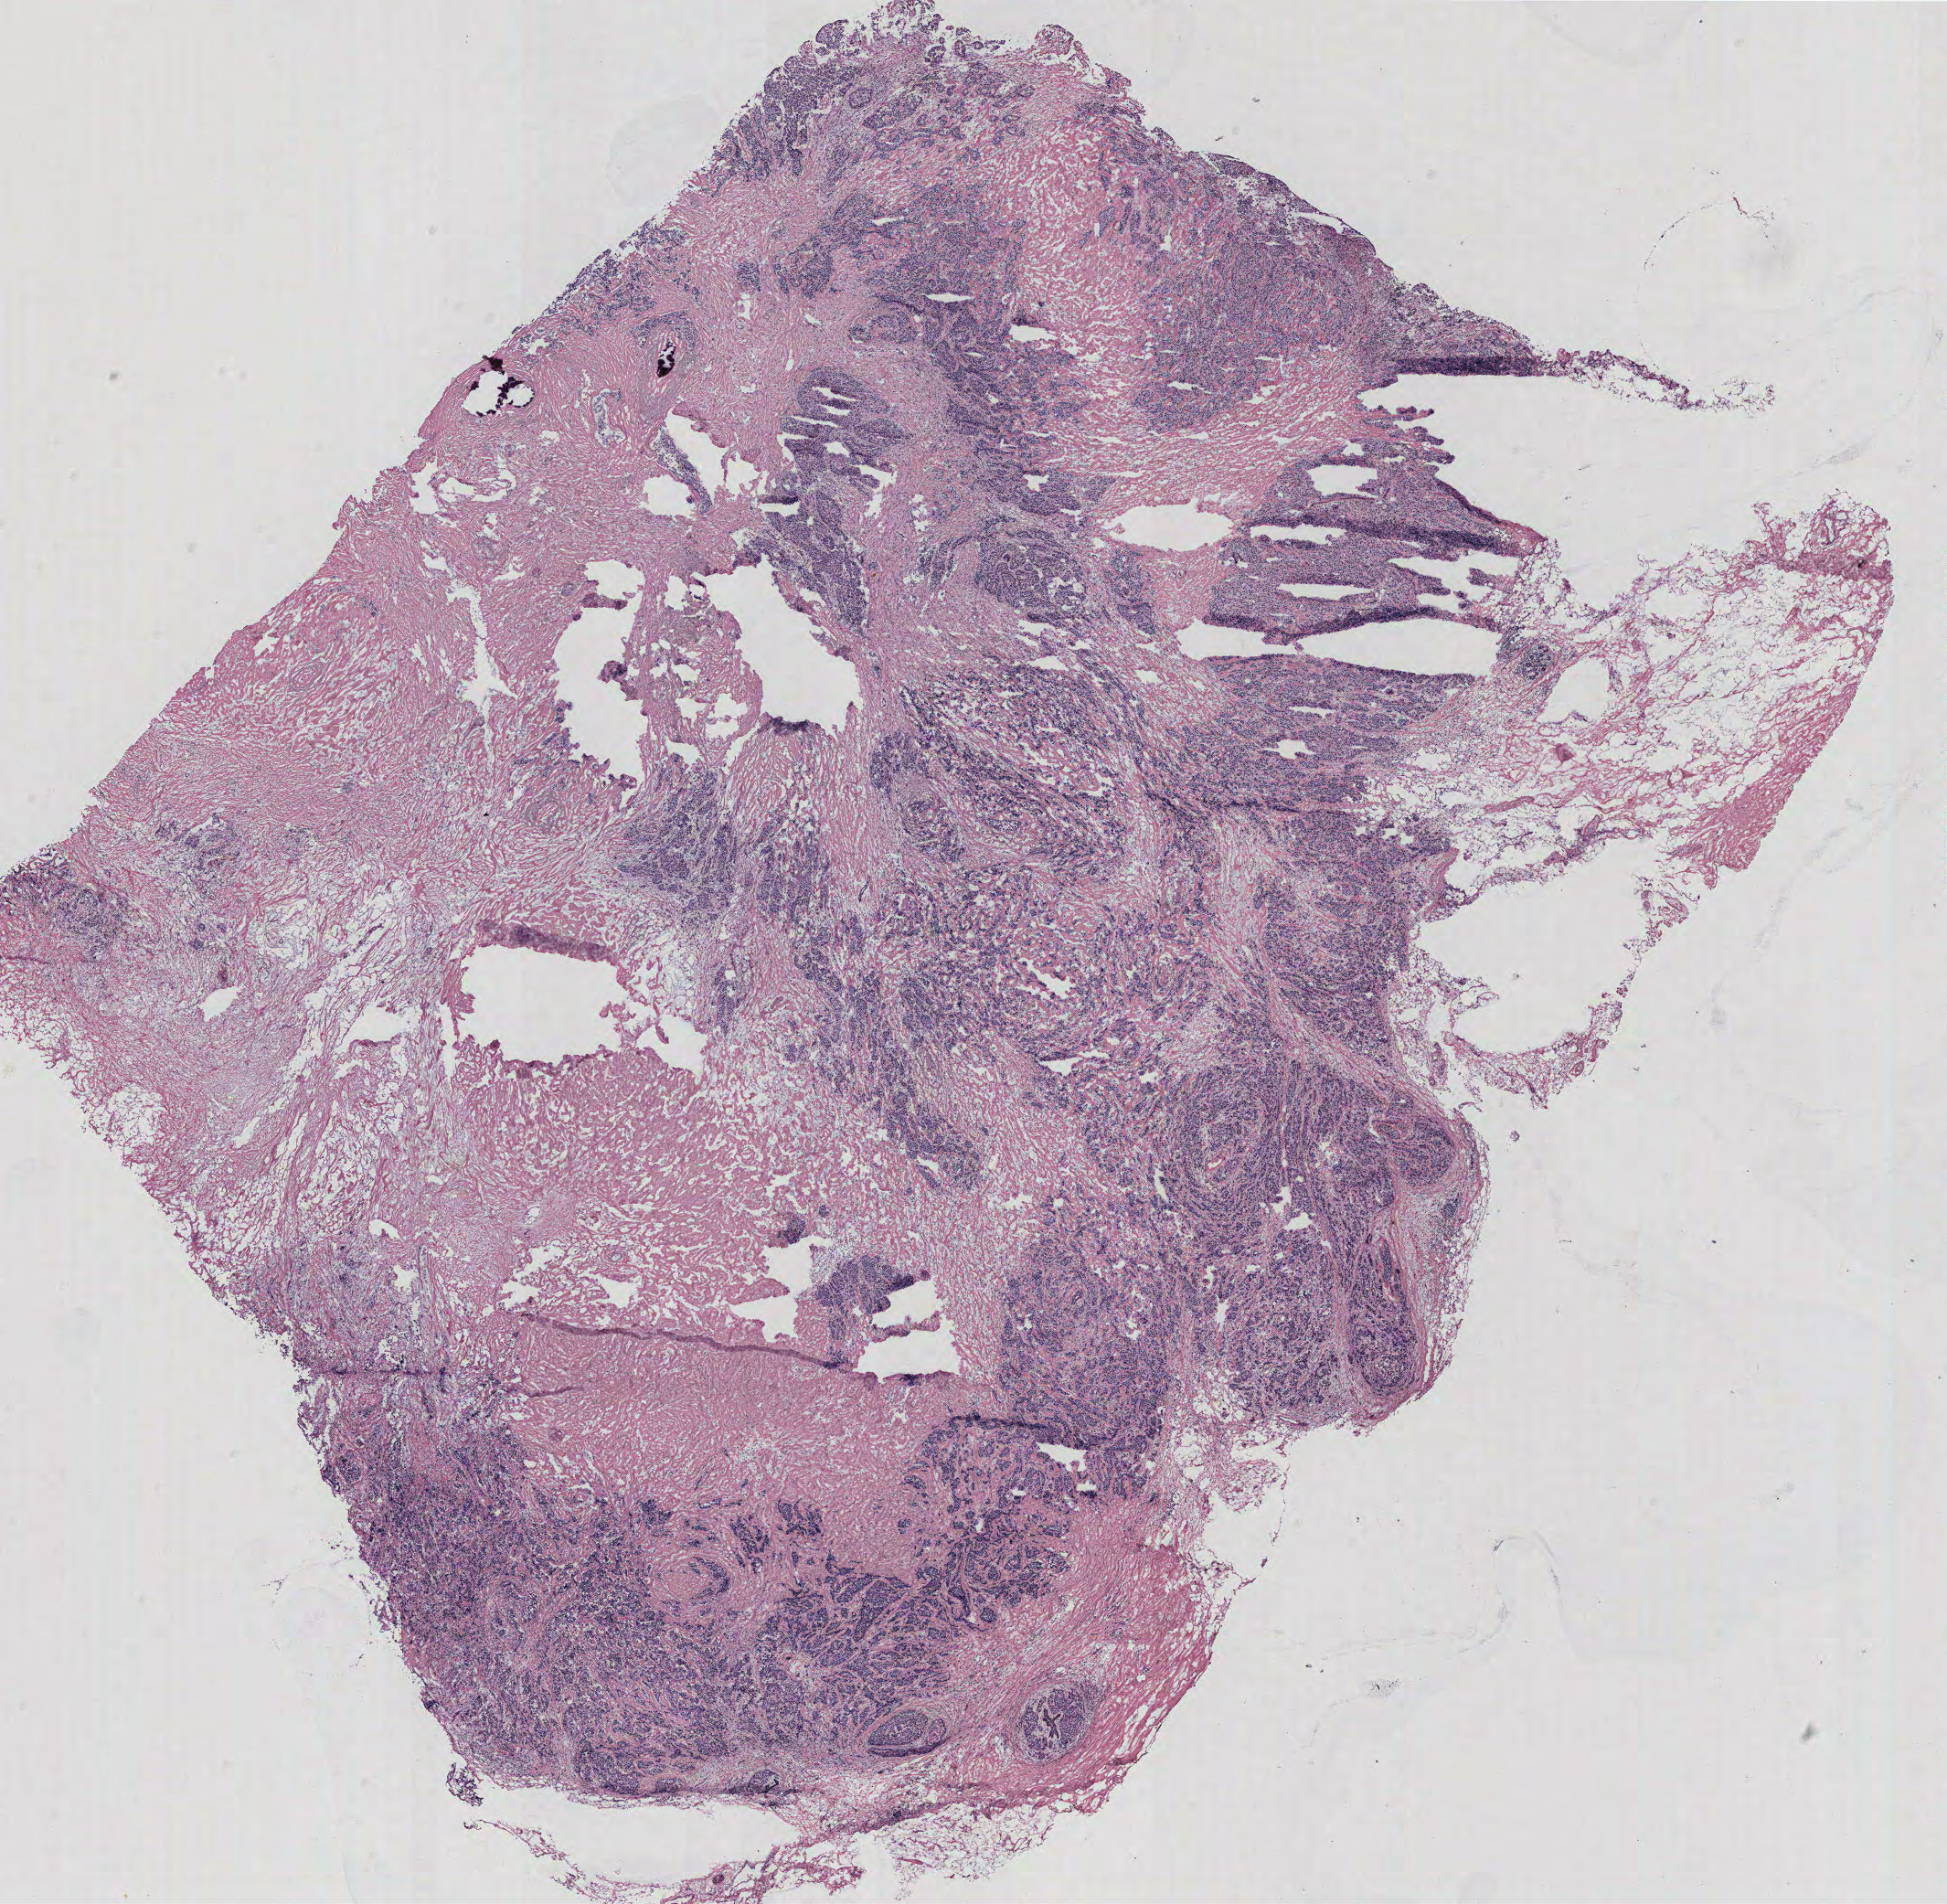
Digitized H&E-stained tissue section (whole slide), a low-resolution overview of the entire scanned area, about 17.0 x 16.7 mm. Breast, tissue type not recorded. Patient: female, age 62 years.
Patient diagnosis: Infiltrating duct carcinoma, NOS.